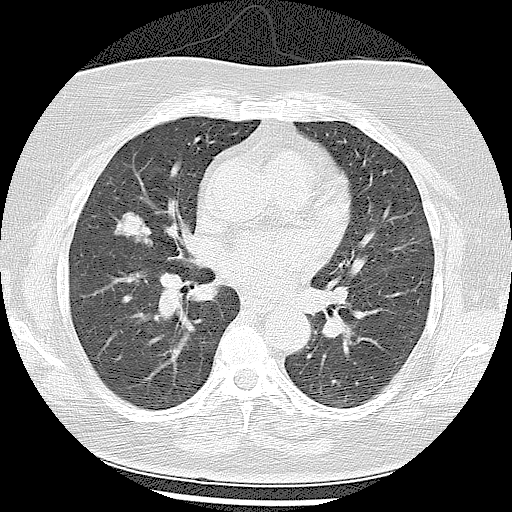
Low-dose screening chest CT, axial slice. Baseline screening round. Lung window (W 1500 / L -600 HU). Lung (sharp) reconstruction kernel (LUNG). 120 kVp. Slice 52 of 102 in the series. Female participant, aged 57 years at enrolment.
- Lesion marked by an expert reader, bounding box (x1, y1, x2, y2) in pixels: (104, 201, 167, 256).
- The screening reader recorded 4 non-calcified nodules or masses ≥4 mm on this exam (right middle lobe, right lower lobe, left lower lobe, left lower lobe); which of them this box marks is not recorded.
- Official screen result: positive, change unspecified: nodule(s) >= 4 mm or enlarging nodule(s), mass(es), or other non-specific abnormalities suspicious for lung cancer.
- Participant outcome: lung cancer diagnosed 87 days after this screen — adenocarcinoma, NOS, right middle lobe, well differentiated (G1), stage IA (AJCC 6th edition), 21 mm at pathology.